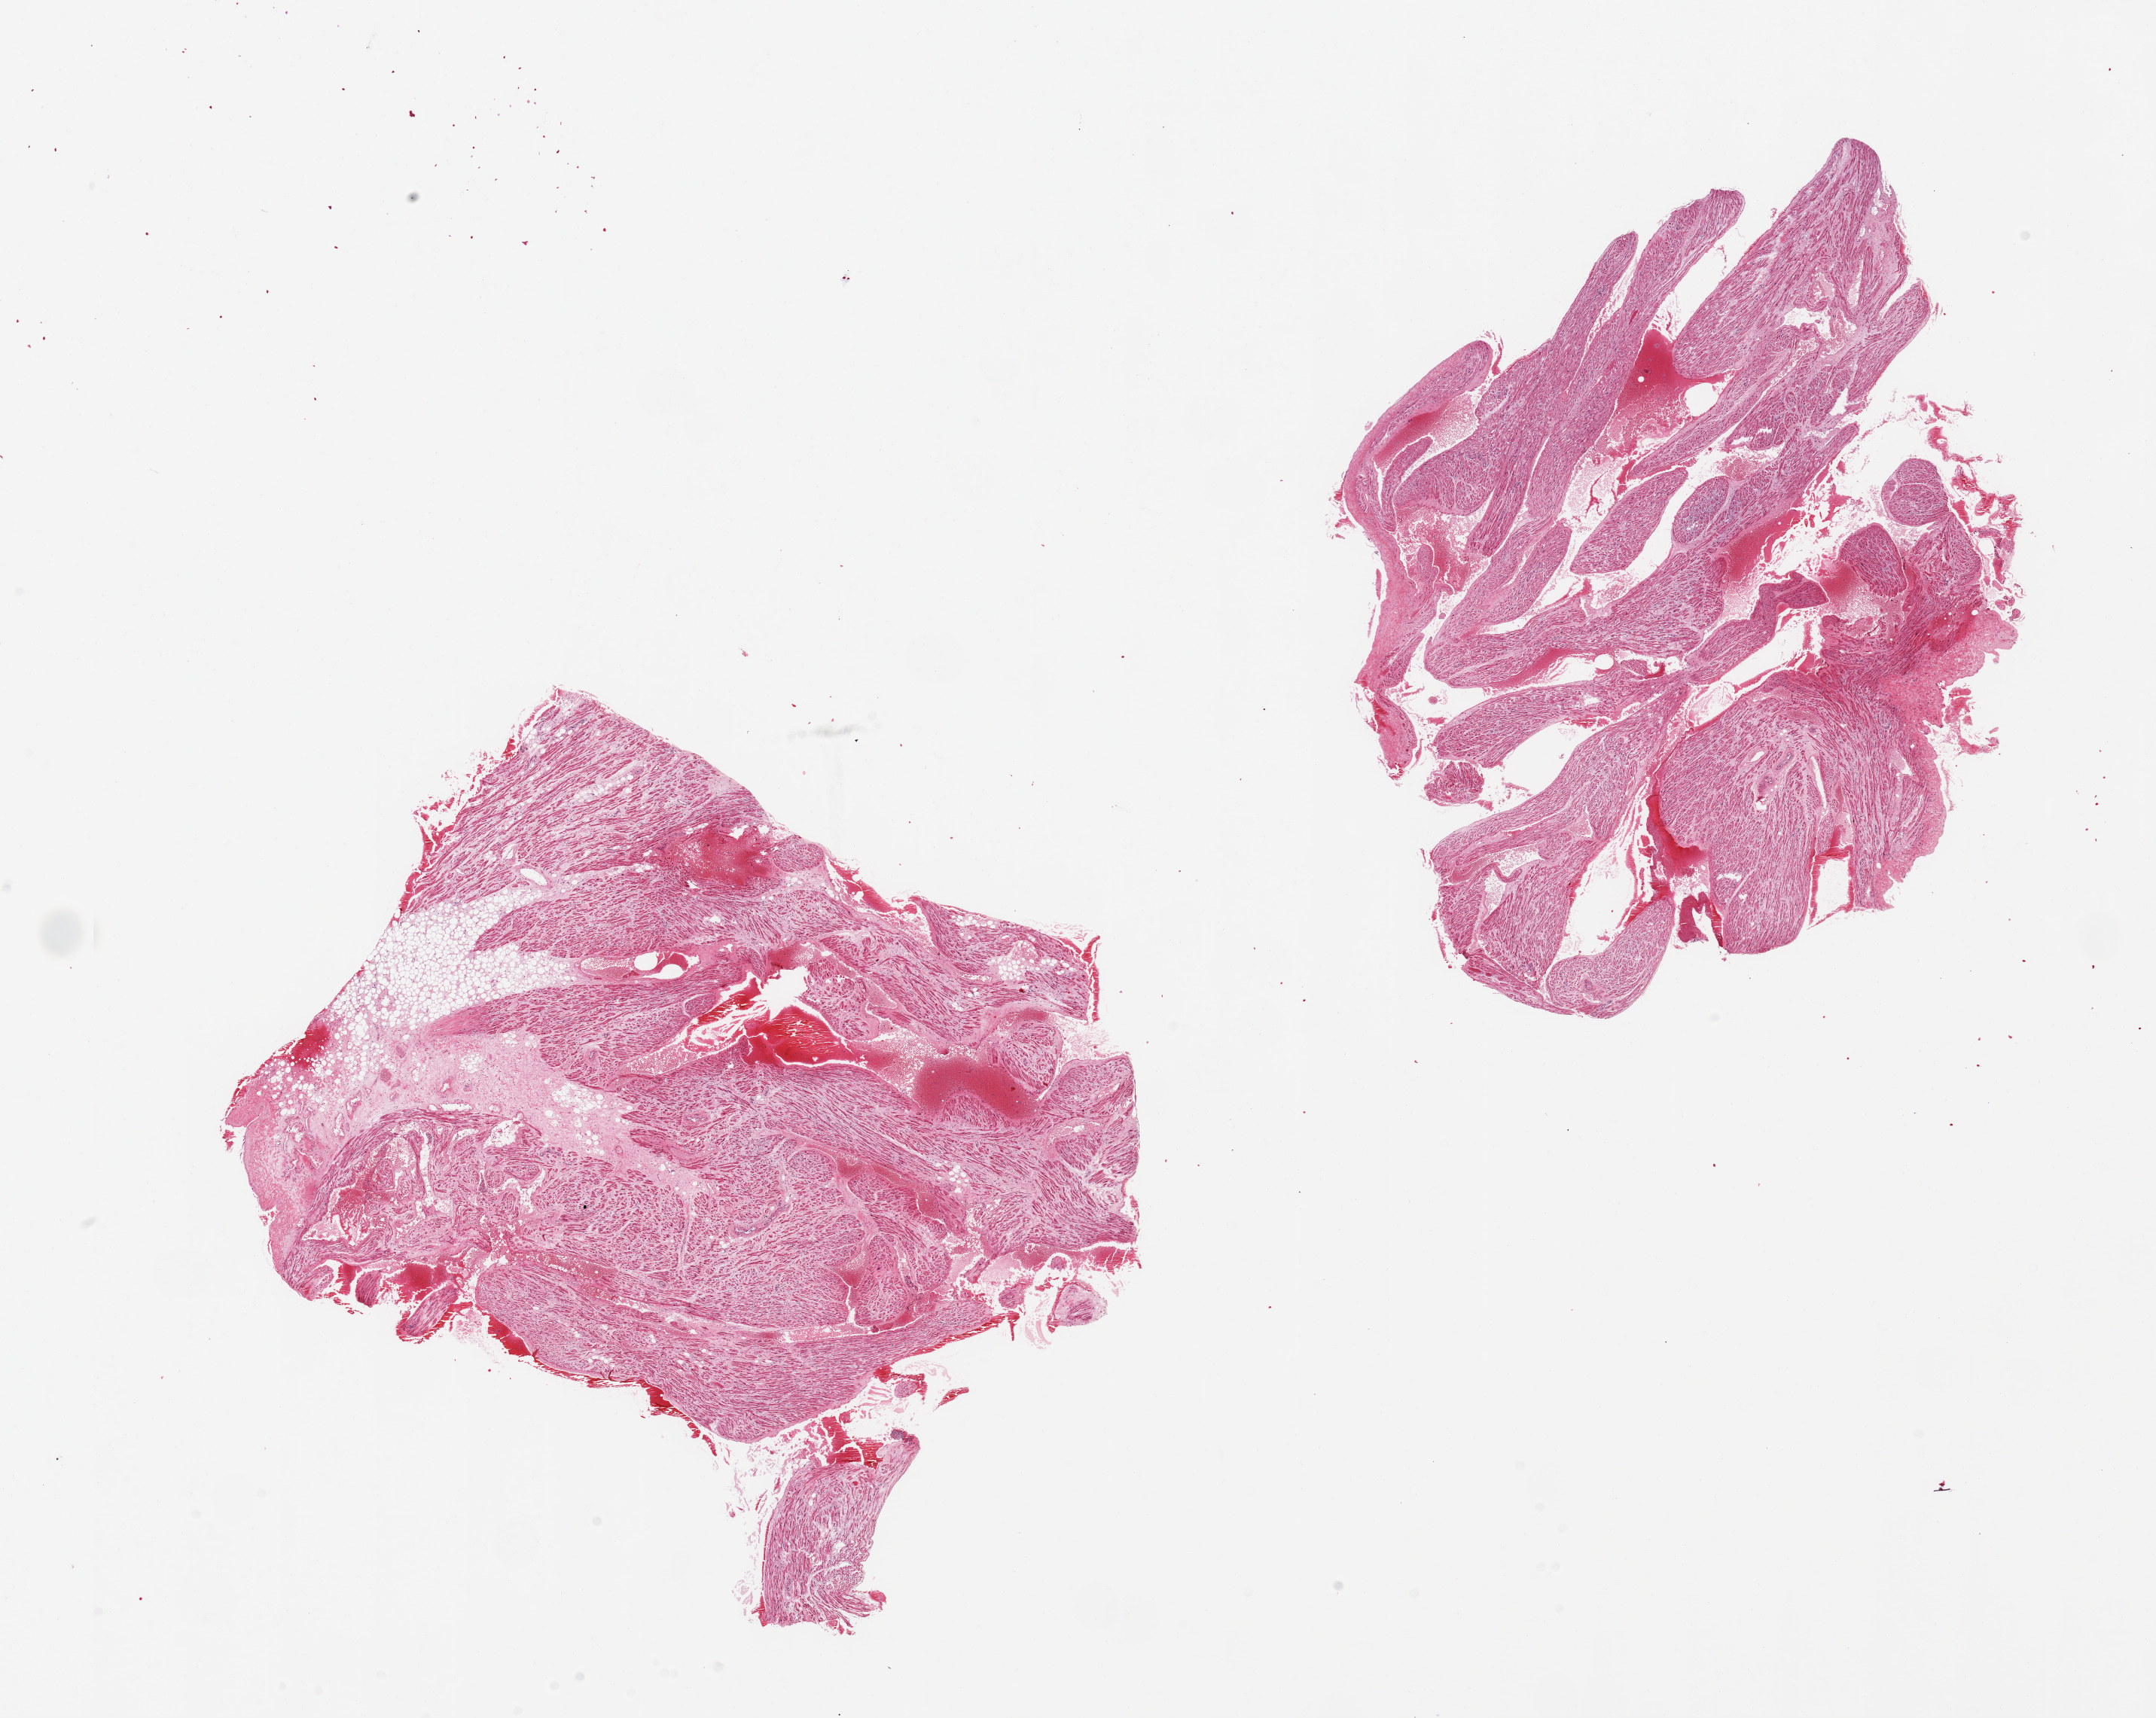
Digitized H&E-stained section — shown as a low-resolution overview of the whole scanned area (about 22.6 x 18.0 mm, slide scanned at 20x); PAXgene-fixed paraffin-embedded (PFPE) section; sampled site (target tissue): auricular appendage; donor tissue sample.
Review note (as recorded): 2 pieces, 8x7 & 7x7mm.